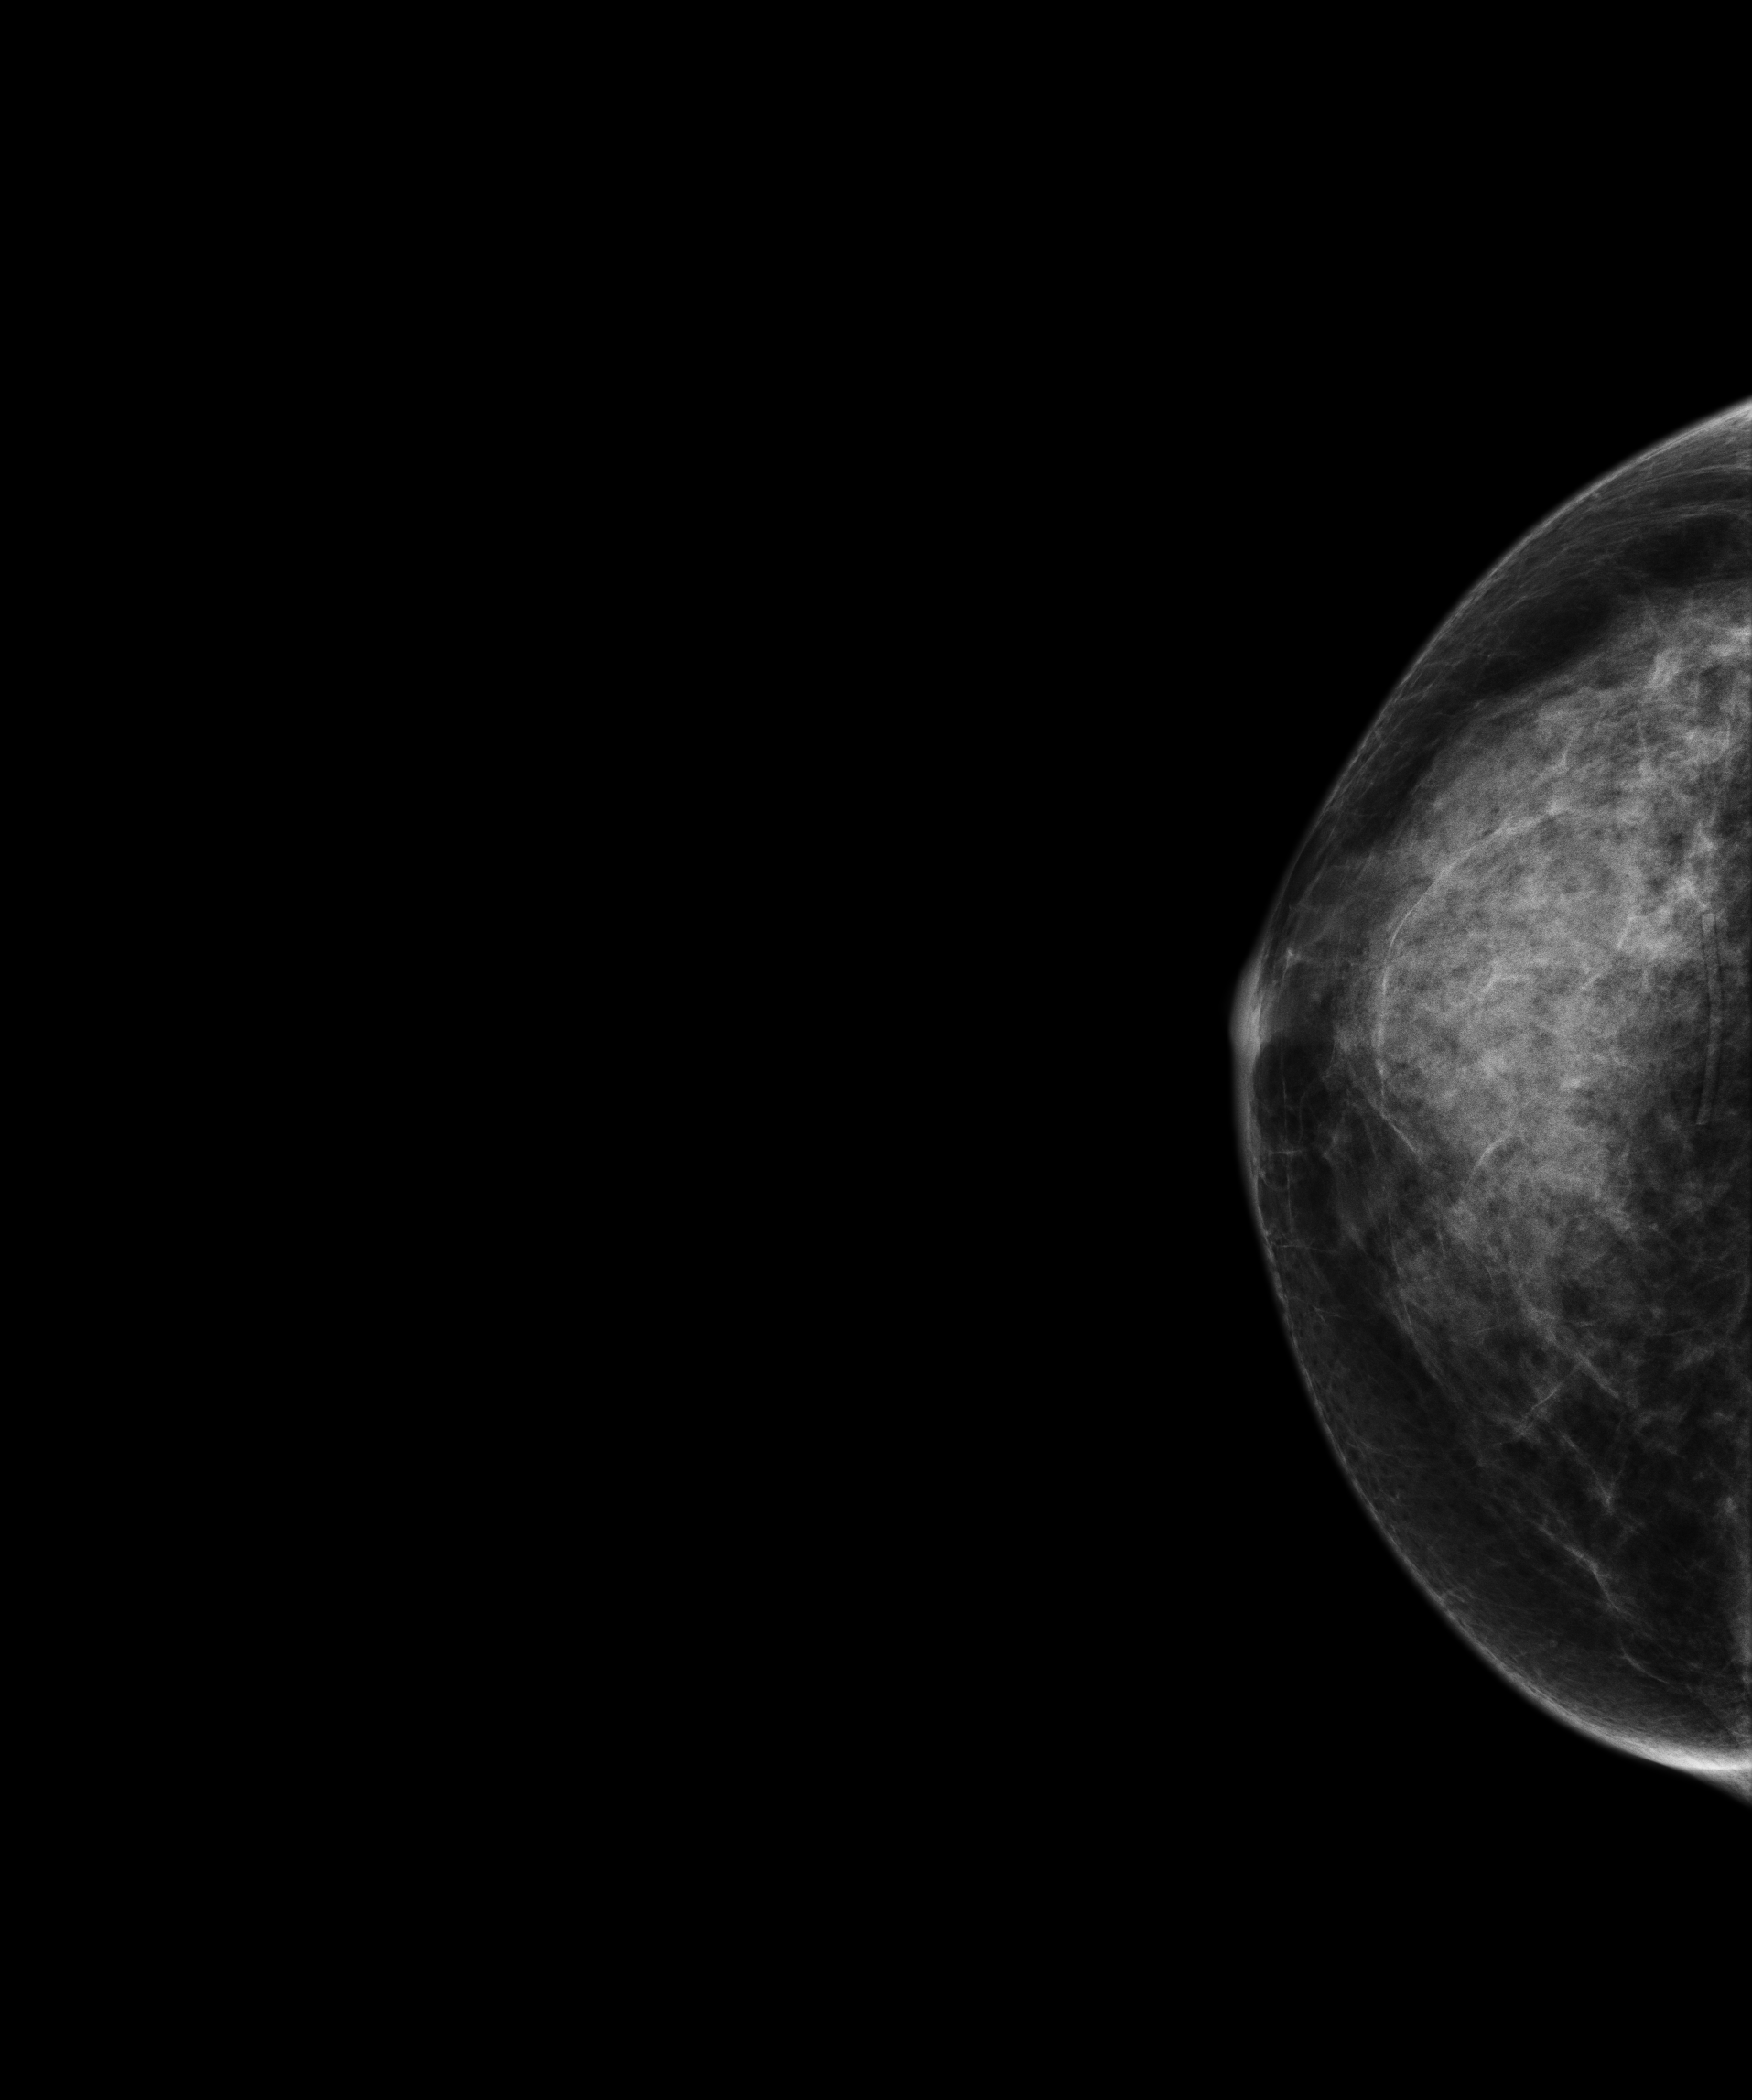
Digital mammogram (FFDM), right breast, craniocaudal (CC) view, annual screening mammography examination, compressed breast thickness 48 mm, system: Senographe Essential ADS_56.21.3. Patient: female, 55 years.
BI-RADS breast density category at the screening exam (both breasts, scale 1–4): 4. Final BI-RADS category for the screening round (tomosynthesis exam, both breasts): category 1. Recall: no recall after this screen.